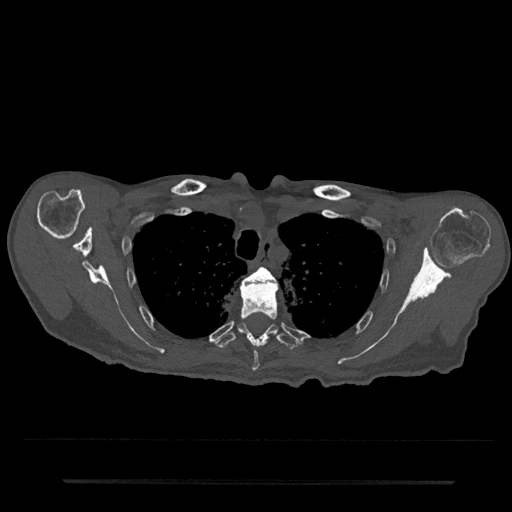
CT including the spine, one axial slice. 120 kVp. Bone window (W 1800 / L 400 HU). 512 × 512 image matrix, field of view 427 × 427 mm. Patient: male, 74 years. Case-level facts recorded for this patient, not image findings: primary cancer: prostate.
Annotated regions visible in this slice (semi-automatically segmented with operator editing):
- T3 vertebra: bounding box <242,267,277,286> (left, top, right, bottom; pixels)
- T4 vertebra: <240,280,278,371>
- T5 vertebra: <214,323,300,350>